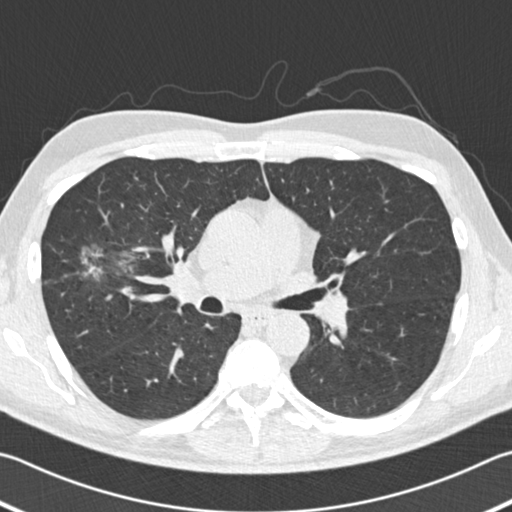
Low-dose screening chest CT, axial slice; second annual screen; lung window (W 1500 / L -600 HU); standard (soft-tissue) reconstruction kernel (B30f); 120 kVp; slice 72 of 182 in the series. Male participant, aged 56 years at enrolment. Former smoker at enrolment.
- Lesion marked by an expert reader, bounding box [x1, y1, x2, y2] px = [51, 234, 142, 300].
- The exam's reader record, not a measurement of the box and not confirmed to be the same lesion: non-calcified nodule or mass ≥4 mm, right upper lobe, 18 × 14 mm, spiculated (stellate) margins, soft tissue attenuation, pre-existing on the prior screen: yes; interval growth: yes.